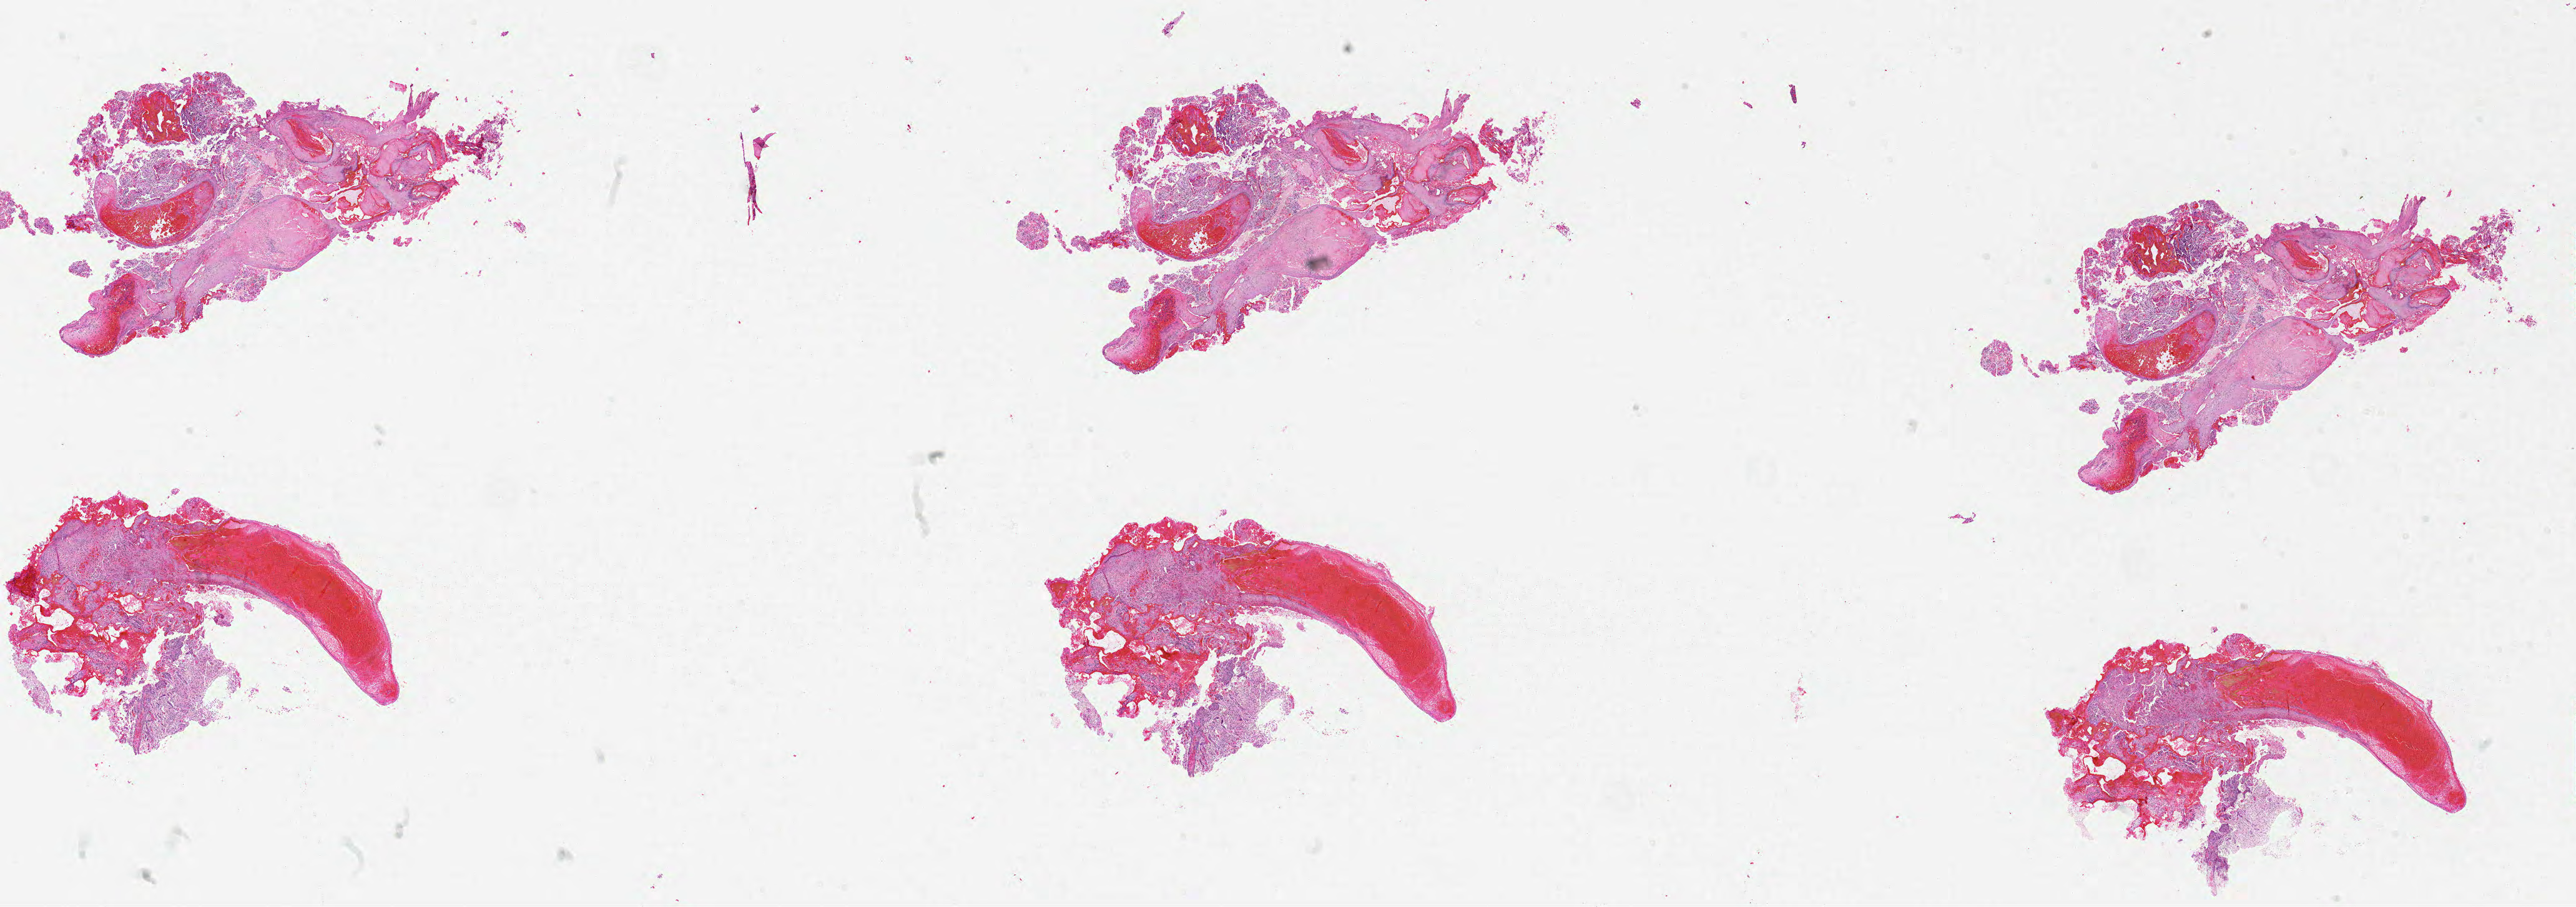
Whole-slide histology image, H&E, shown as a low-resolution overview of the whole scanned area (about 33.0 x 11.6 mm, from a 20x scan); formalin-fixed paraffin-embedded (FFPE) diagnostic section; primary tumour sample from the brain. Patient: male, age at initial diagnosis 46 years.
Histologic diagnosis: Glioblastoma.